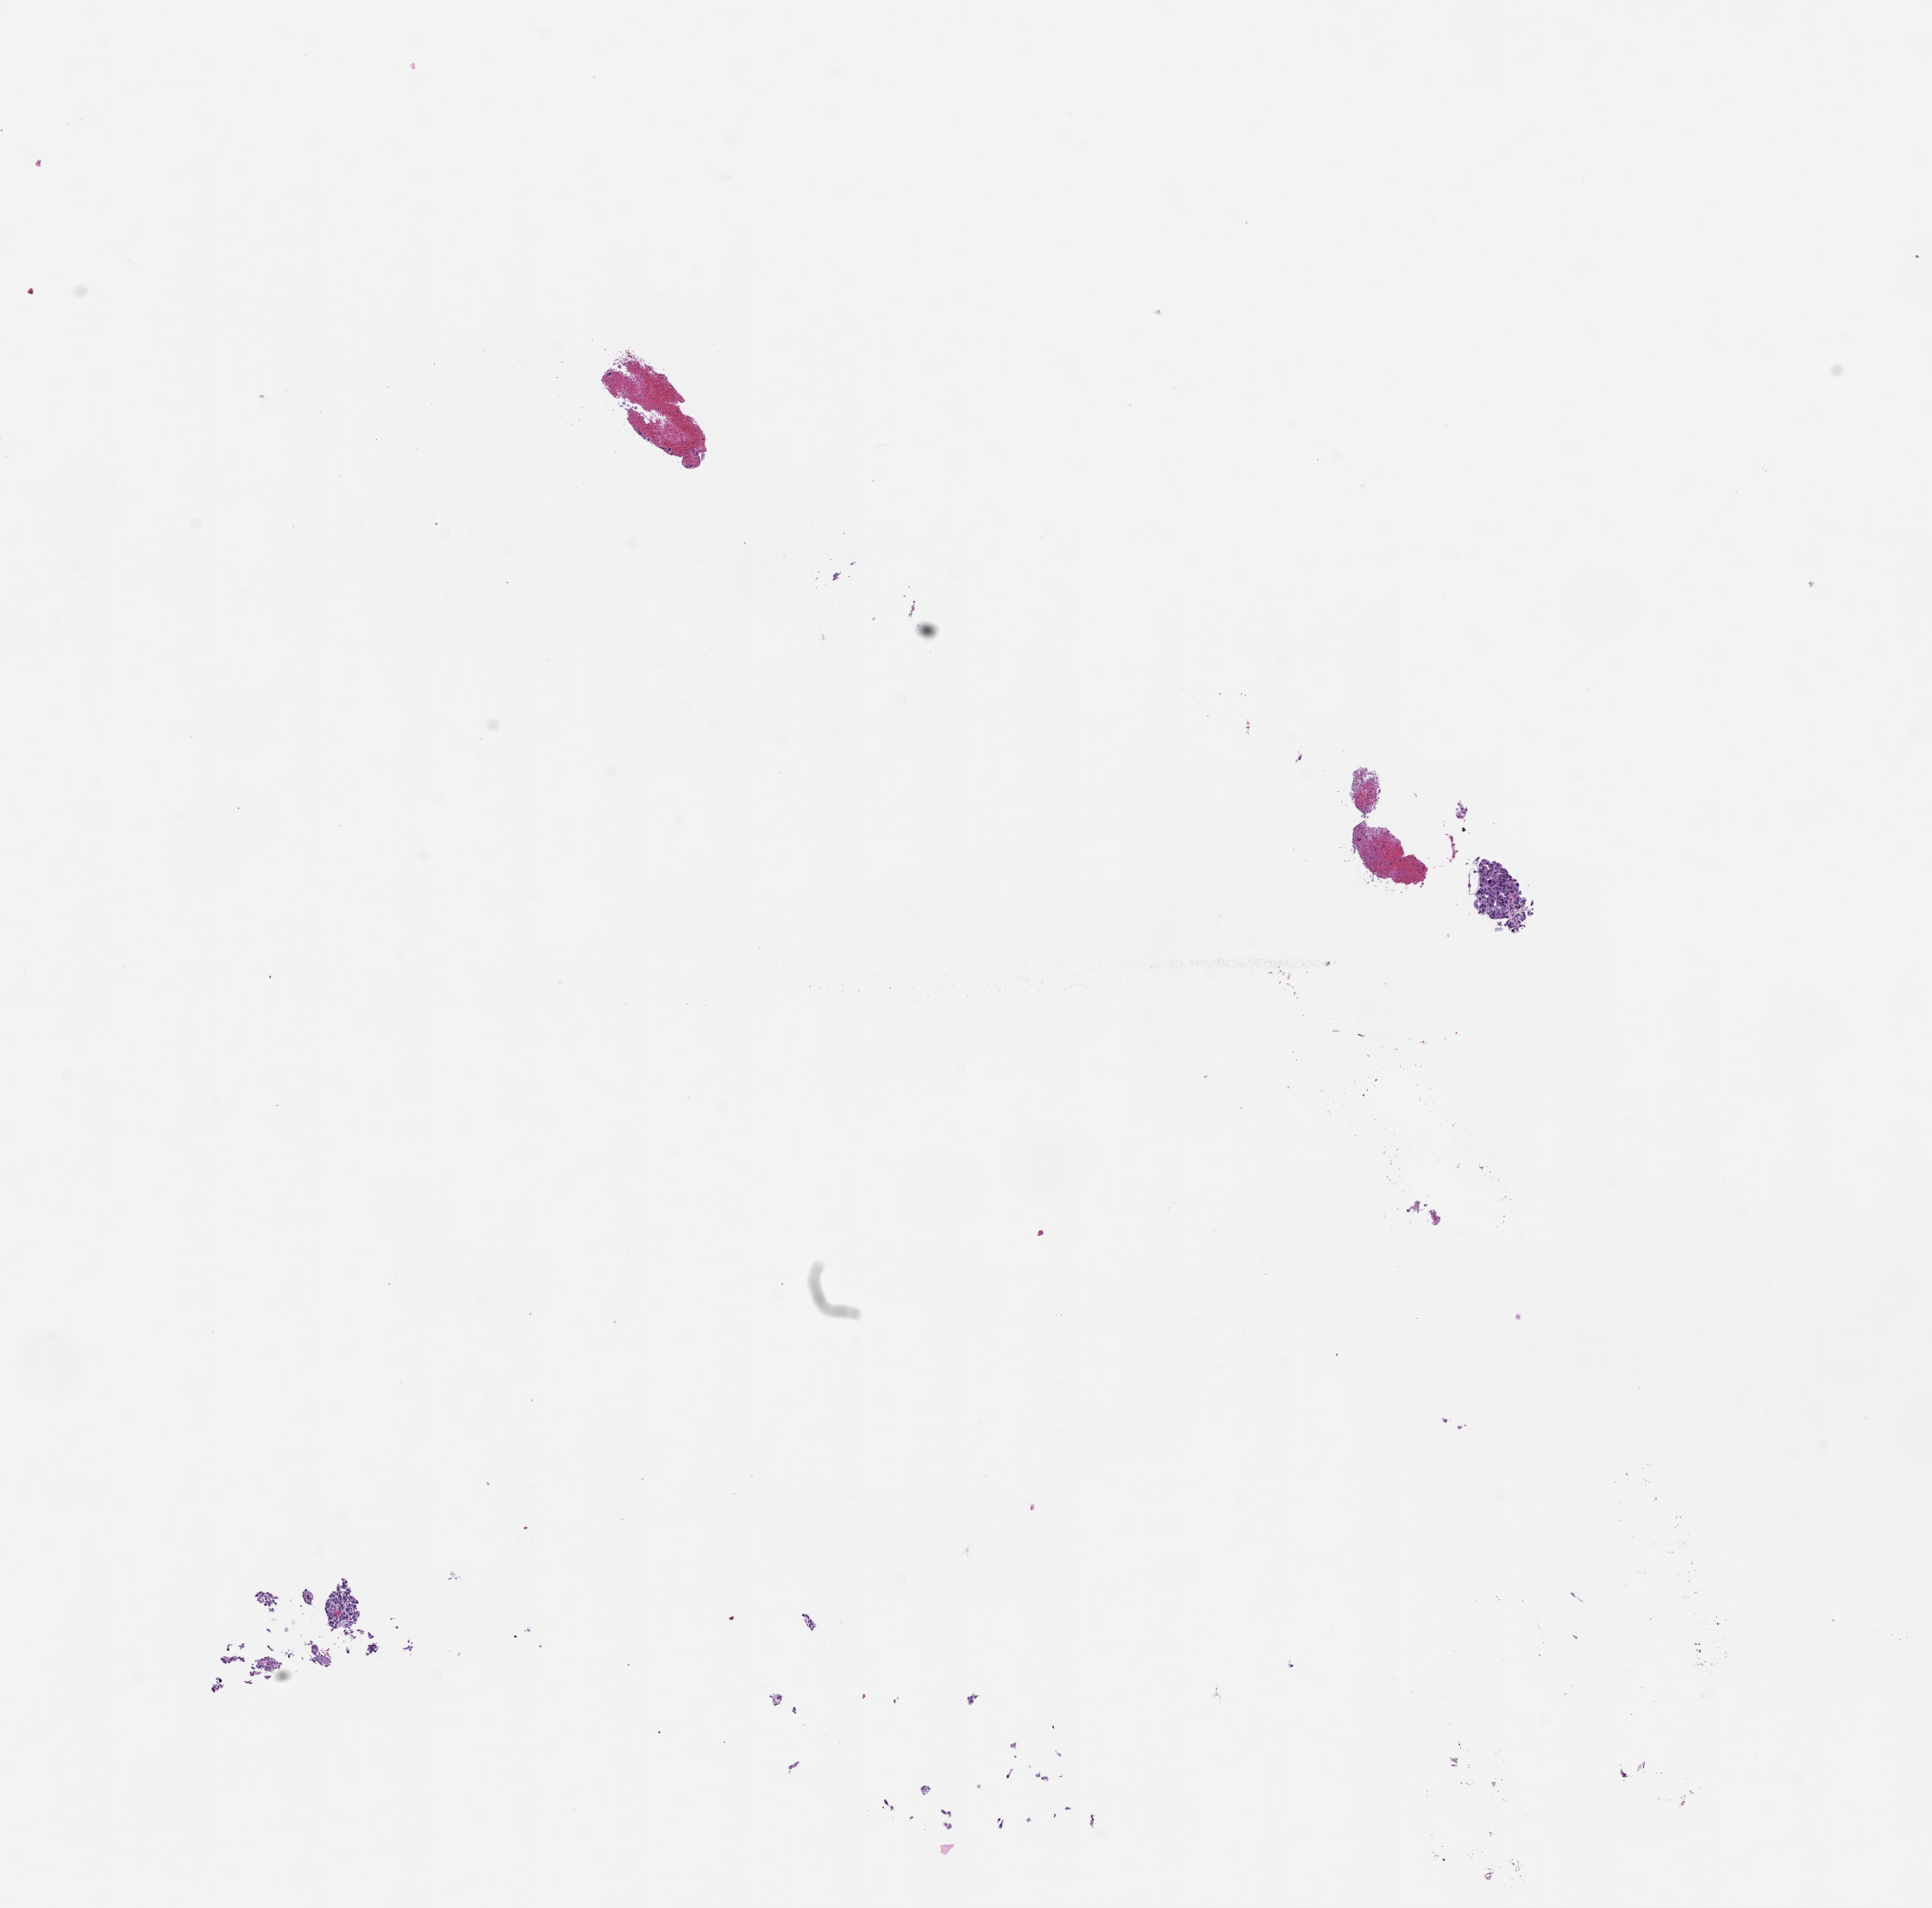
Whole-slide image, H&E stain — low-resolution overview of the scanned area, about 9.0 x 8.9 mm, formalin-fixed paraffin-embedded section. Patient sex: female.
This section: metastasis (sampled organ not recorded). Patient diagnosis (primary): Non-Small Cell Lung Carcinoma.